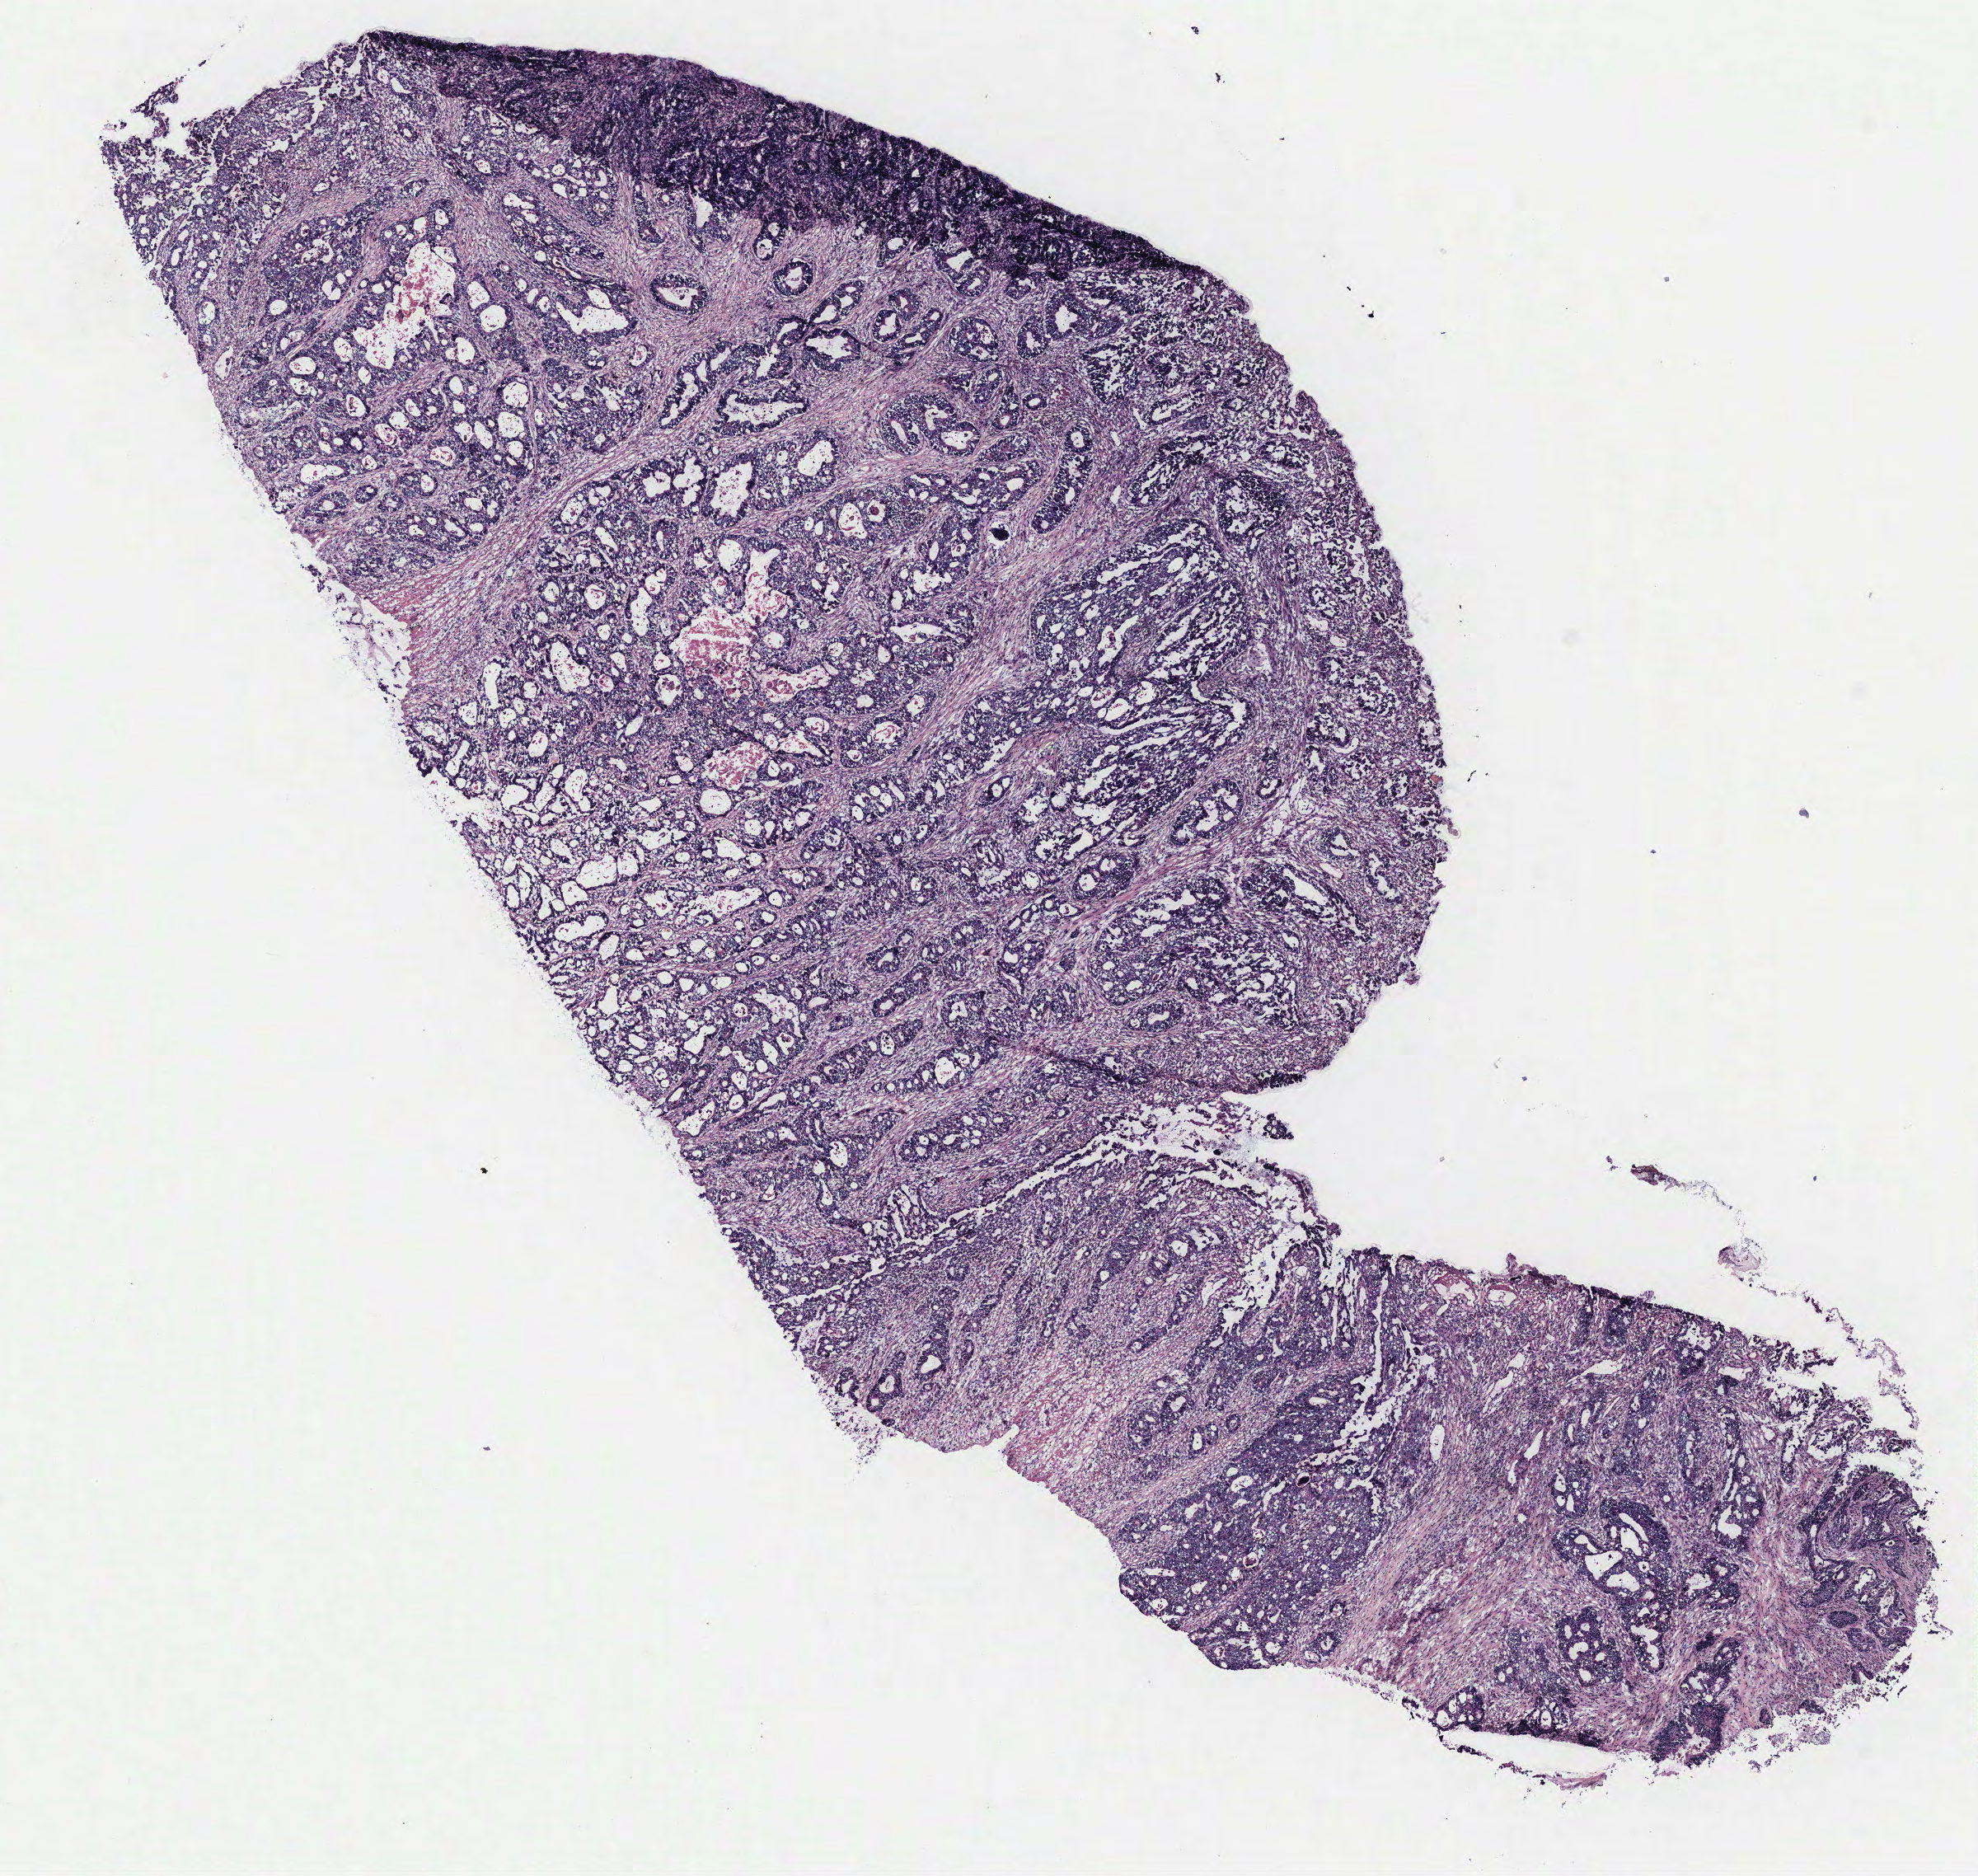
Digitized Hematoxylin and eosin (H&E) stained tissue section (whole slide) — whole scanned area (about 9.6 x 9.1 mm, acquisition: 40x scan) shown as a low-resolution overview. Colon, normal (non-tumour) tissue. Female patient.
- this section: normal (non-tumour) tissue from the same patient
- patient diagnosis: Adenocarcinoma, NOS